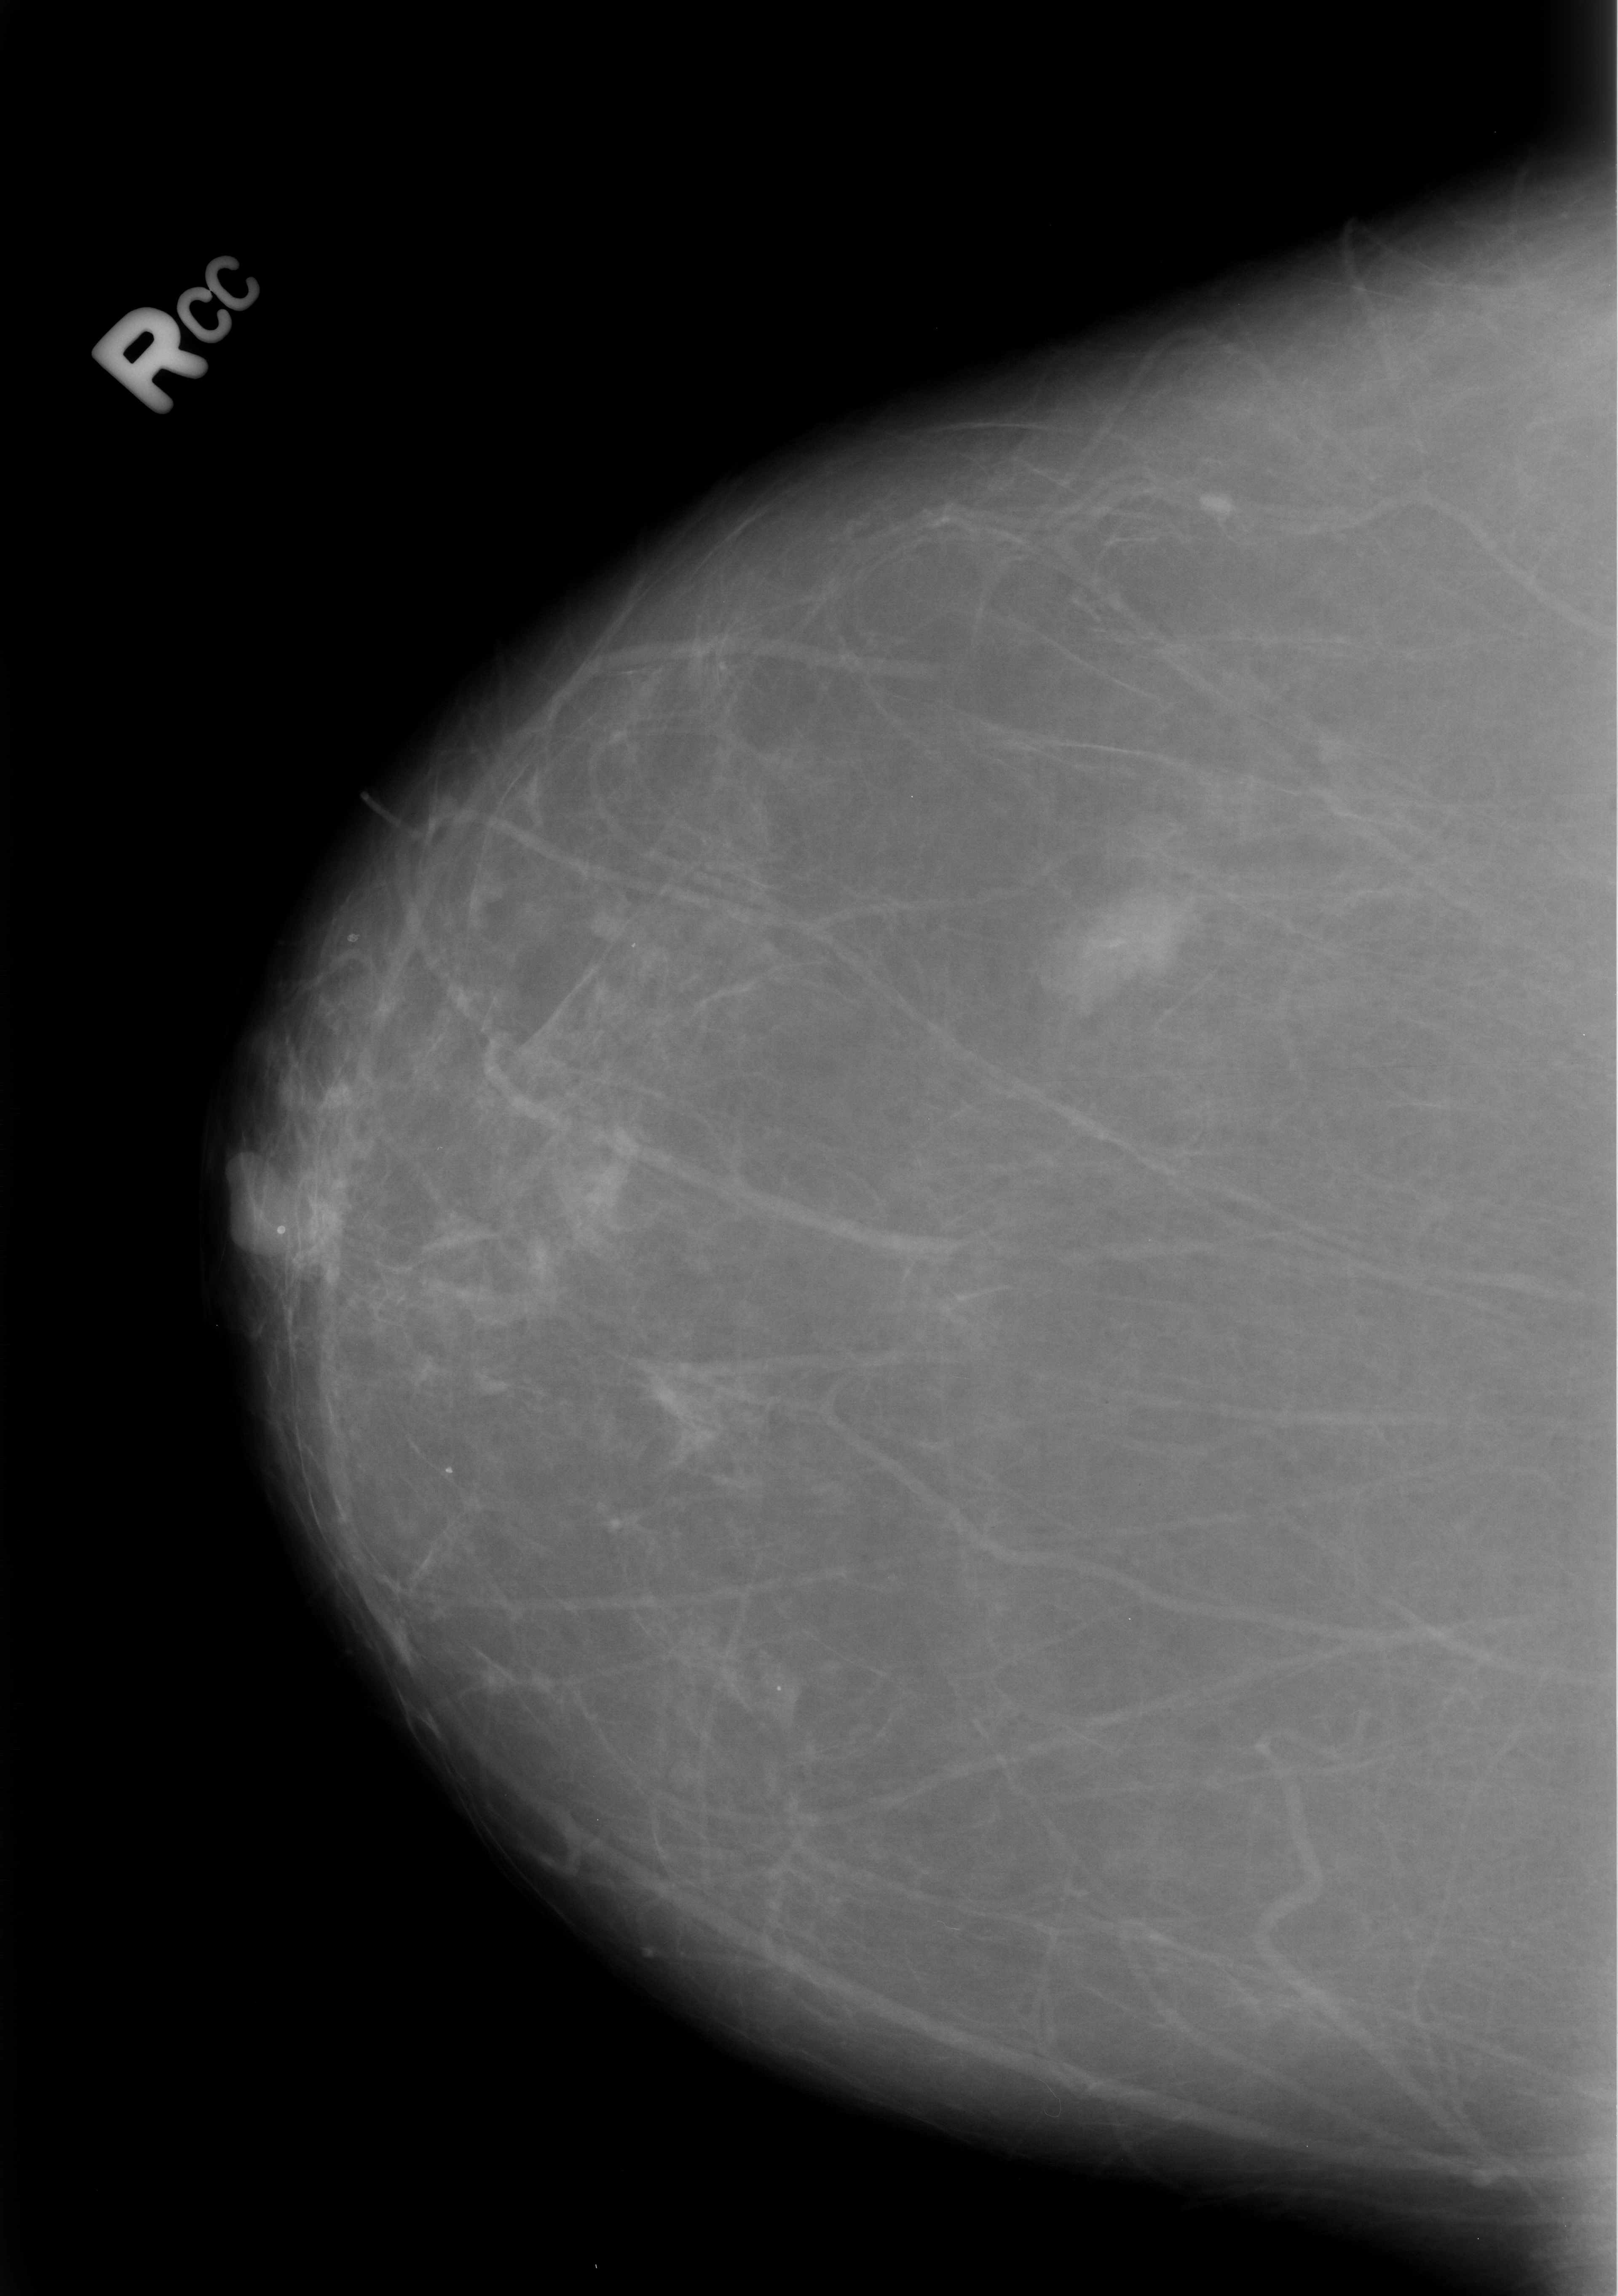
Mammogram (digitized film), right breast, CC view, BI-RADS breast density category 1 (scale 1–4).
Finding: mass, shape lobulated / irregular, margins ill defined; BI-RADS assessment category 4; pathology result (as recorded, not read from the image): benign.